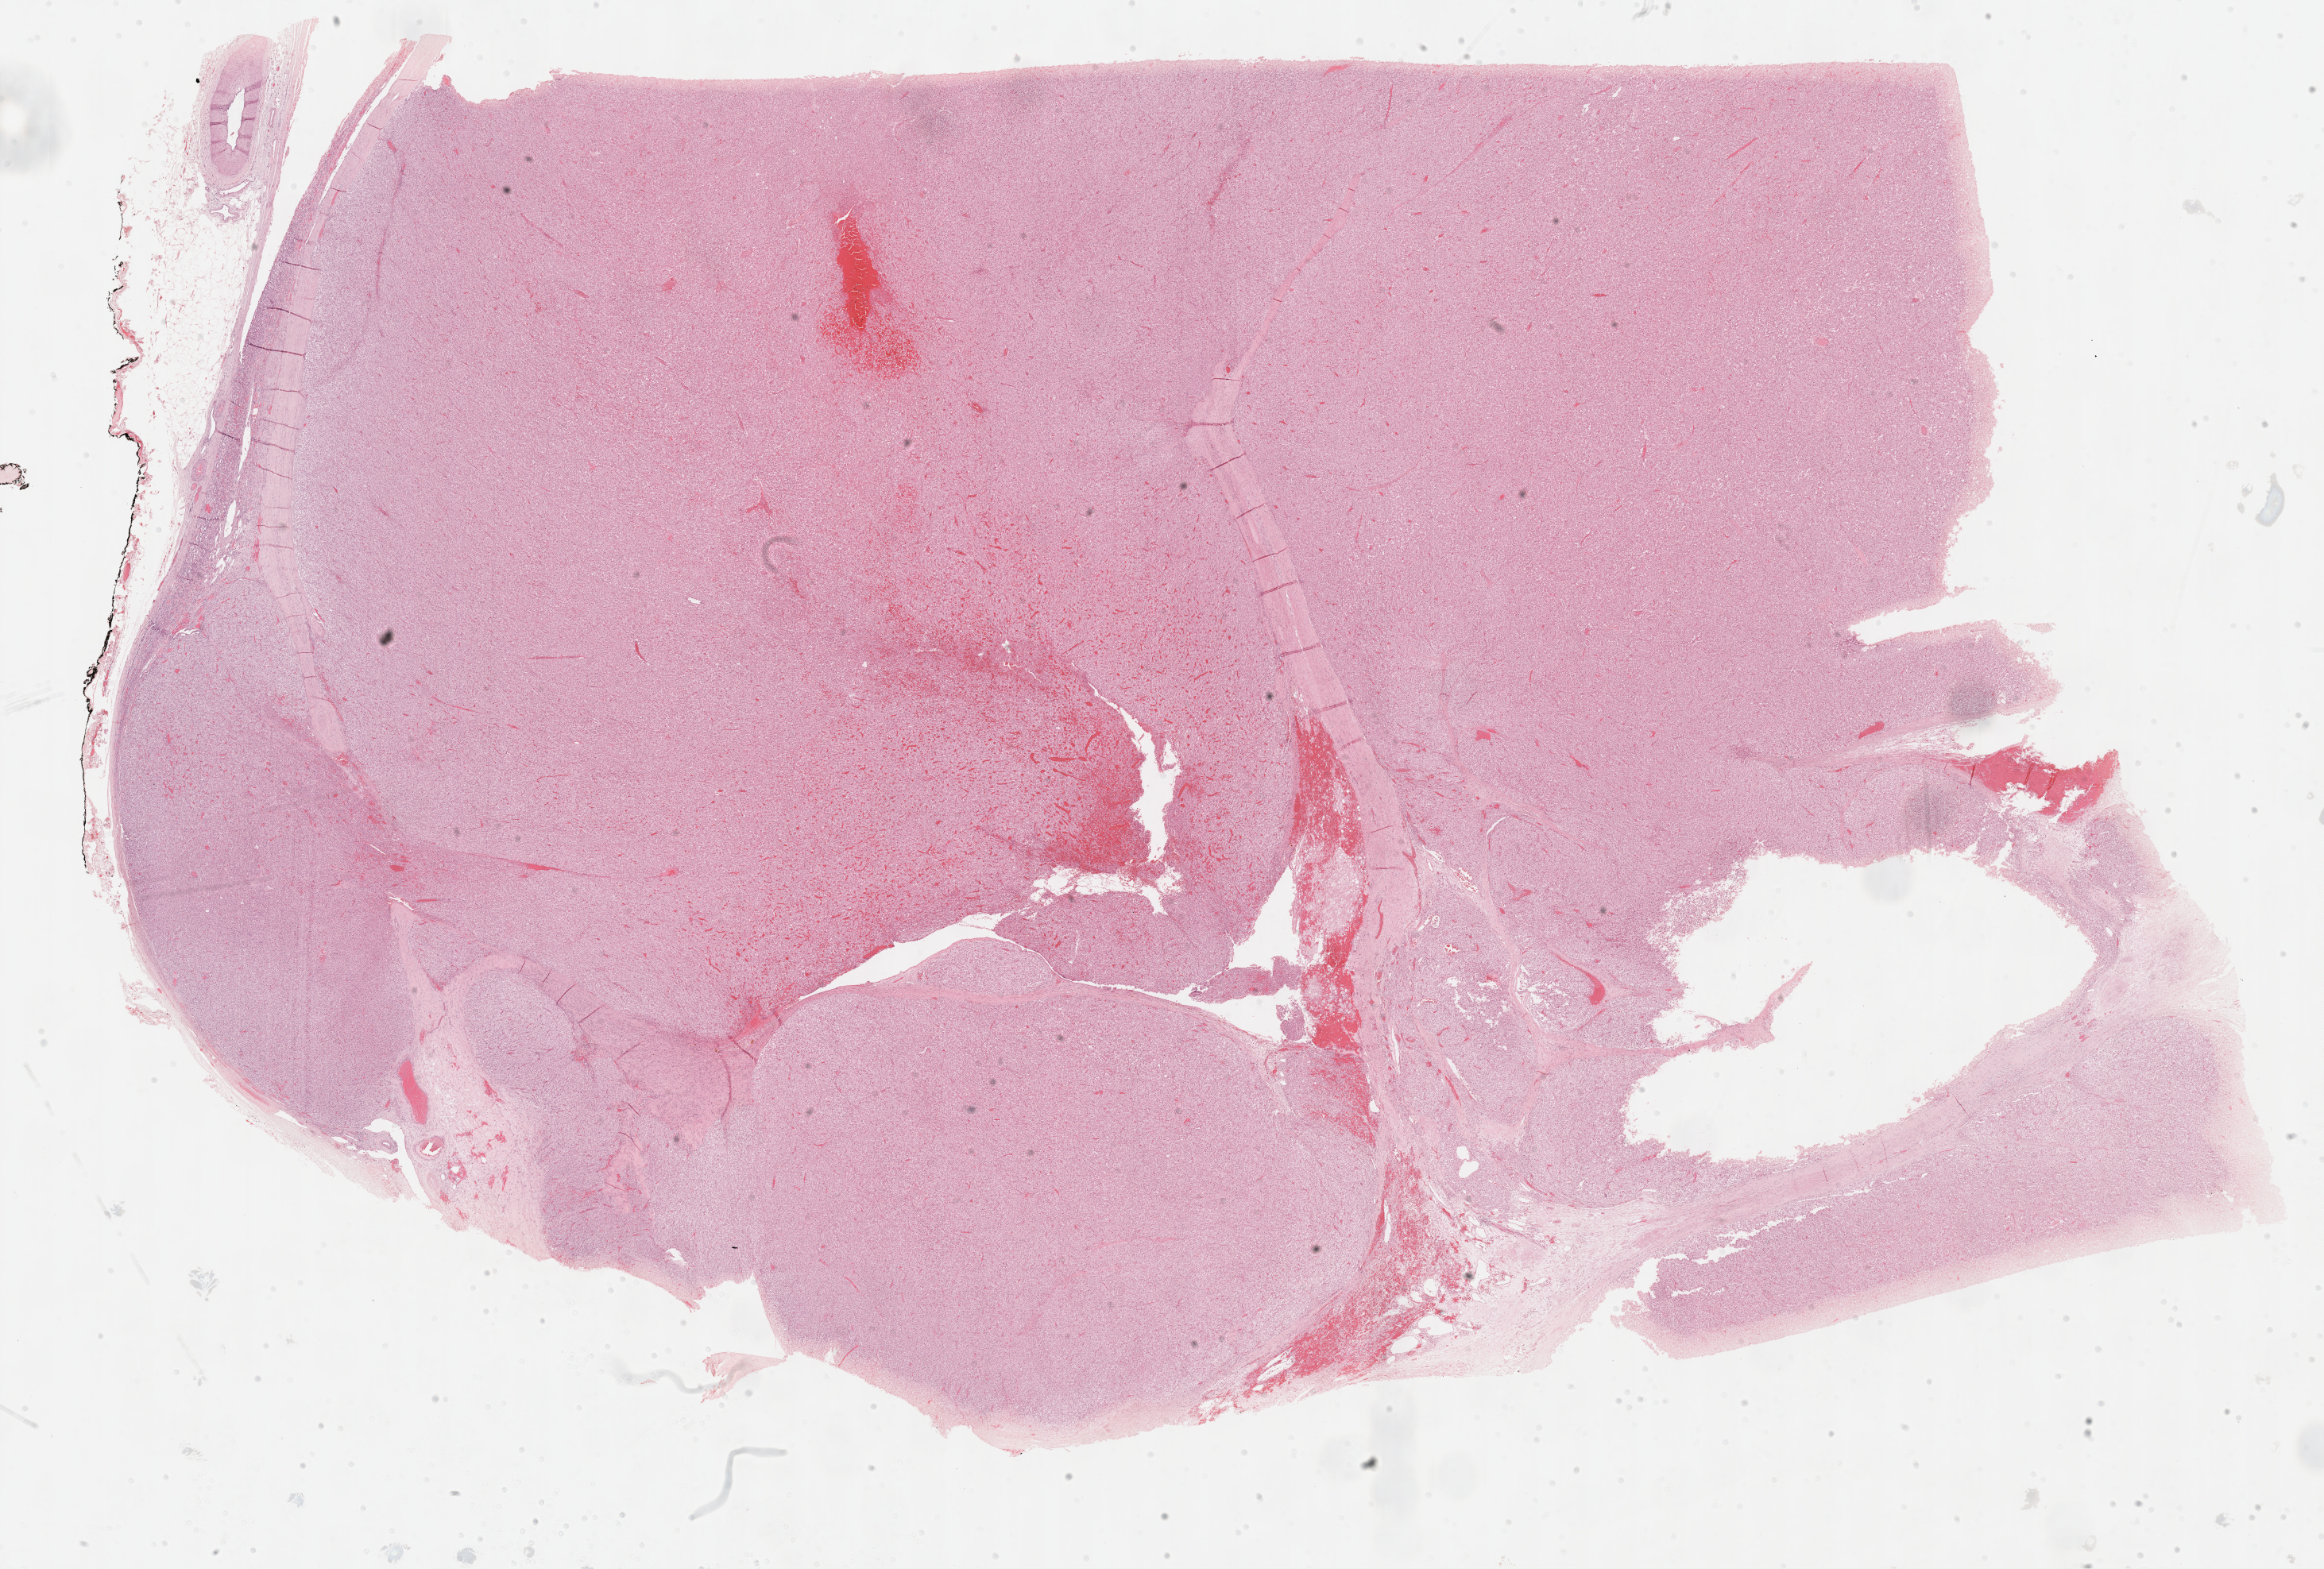
Digitized H&E-stained tissue section (whole slide), shown as a low-resolution overview of the whole scanned area (about 23.7 x 16.0 mm, acquisition: 40x scan); formalin-fixed paraffin-embedded (FFPE) diagnostic section; adrenal cortex, primary tumour sample. Male patient; age at initial diagnosis 48 years.
Histologic diagnosis: Adrenal cortical carcinoma (cortex of adrenal gland). Laterality: left.